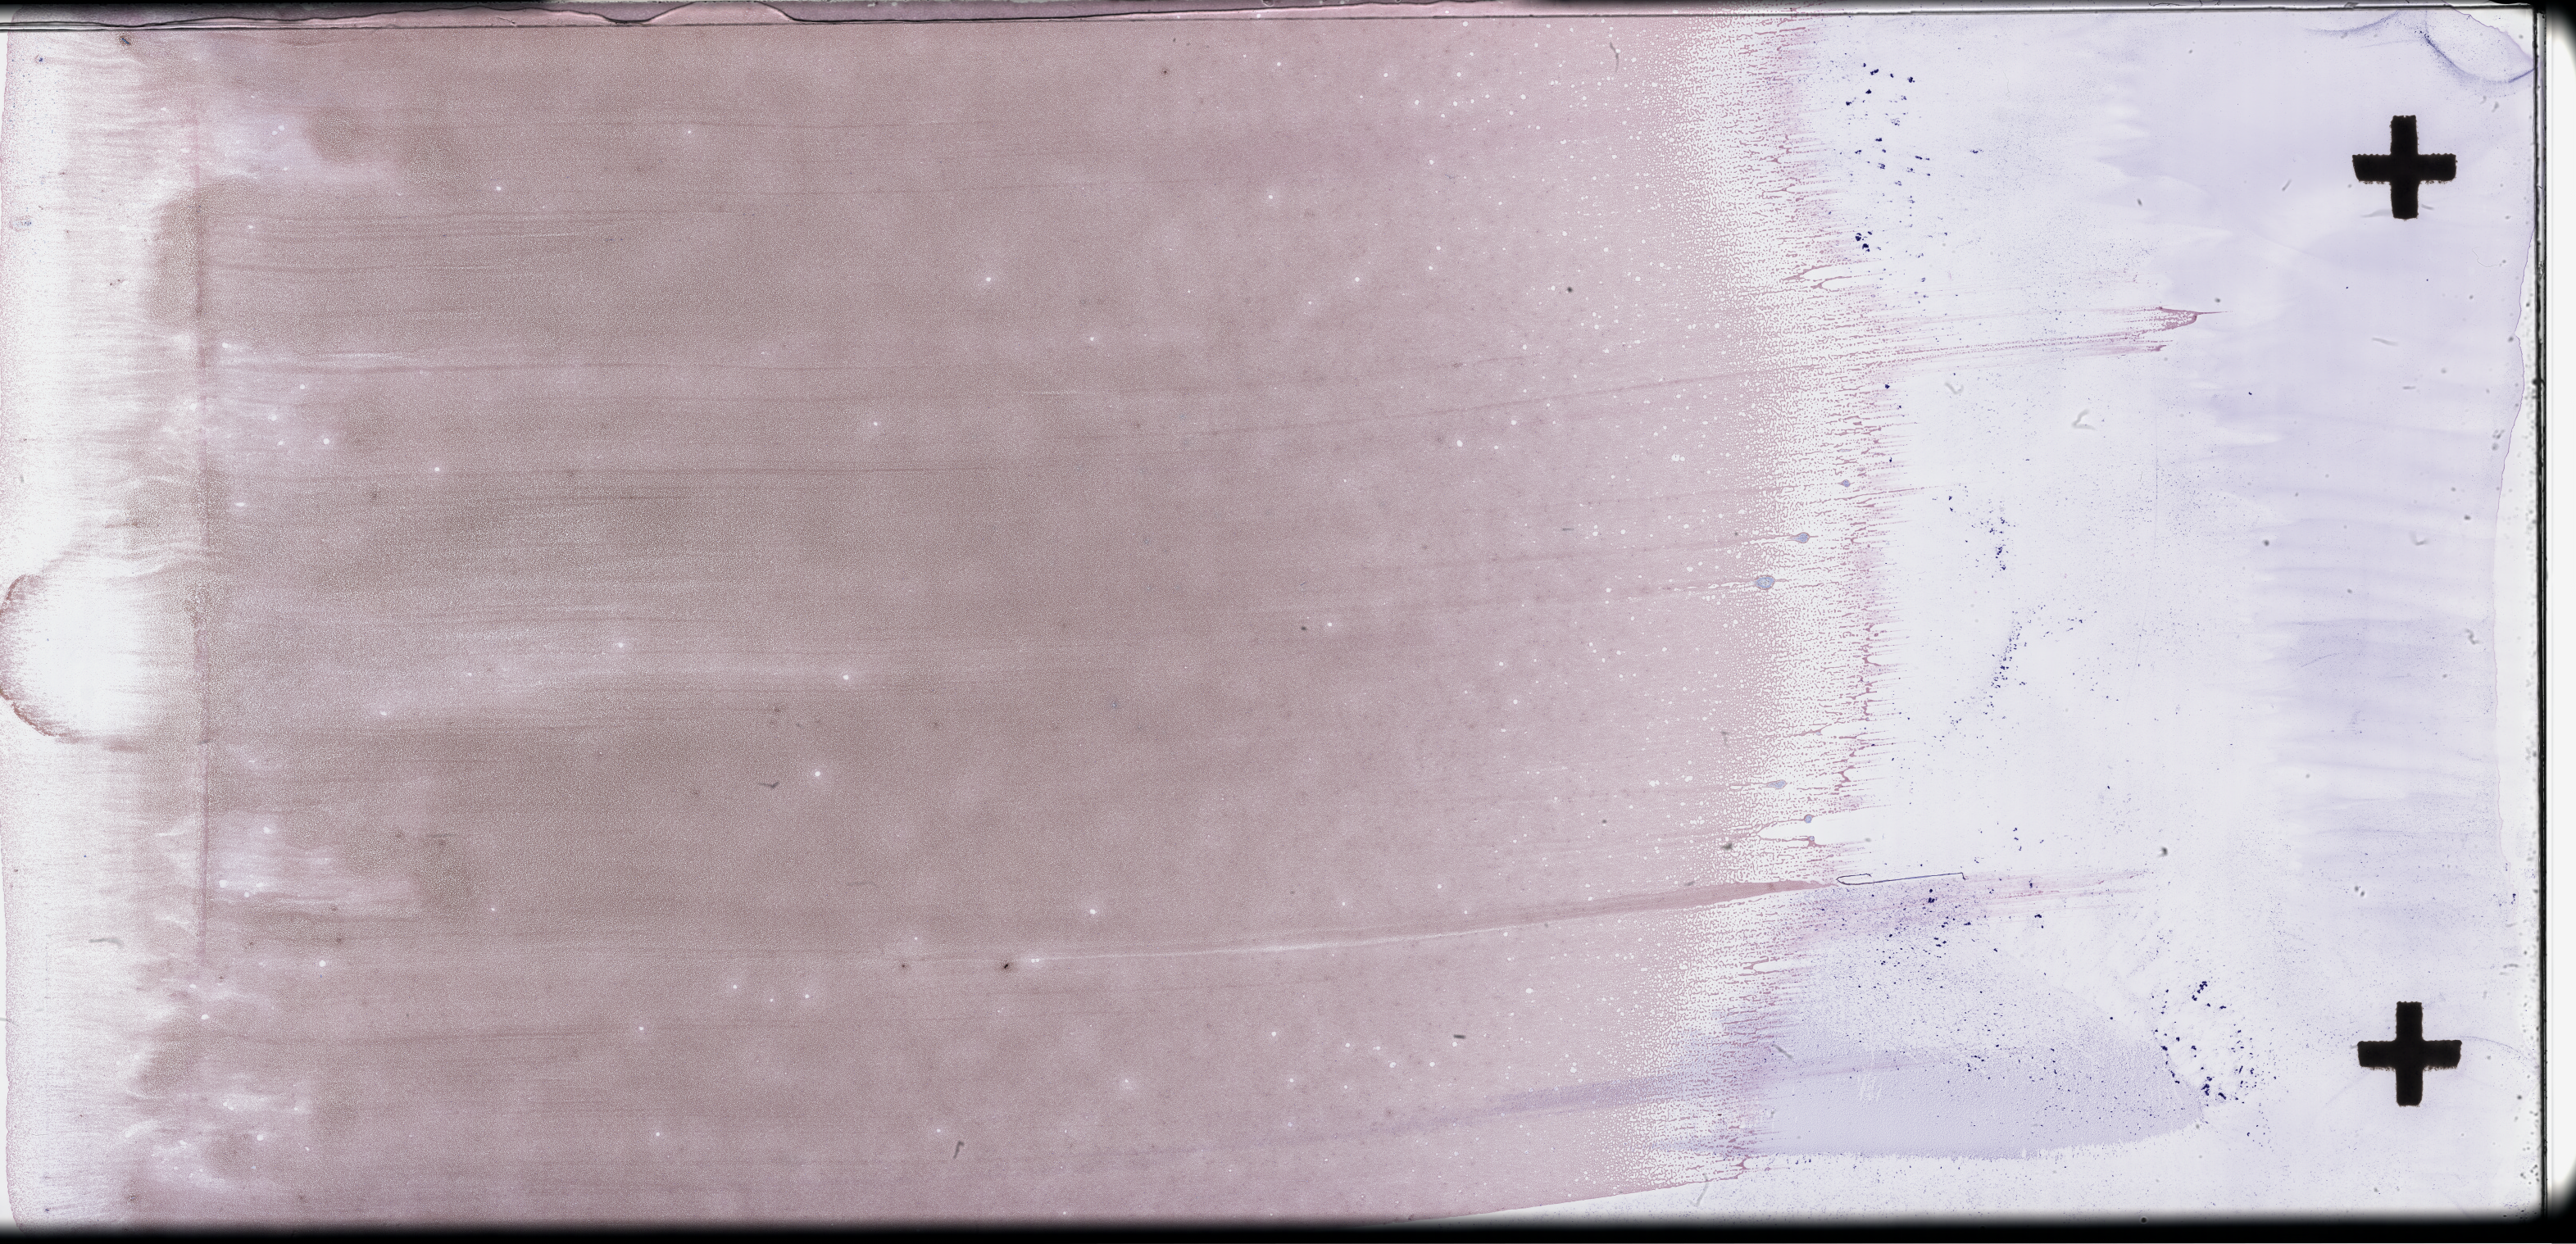
Whole-slide image of a whole blood smear, Wright–Giemsa stain, whole scanned area (about 50.8 x 24.5 mm) shown as a low-resolution overview. Smear from an EDTA sample. Collected at baseline (before treatment). Patient sex: female.
From a patient with: Plasma Cell Myeloma.